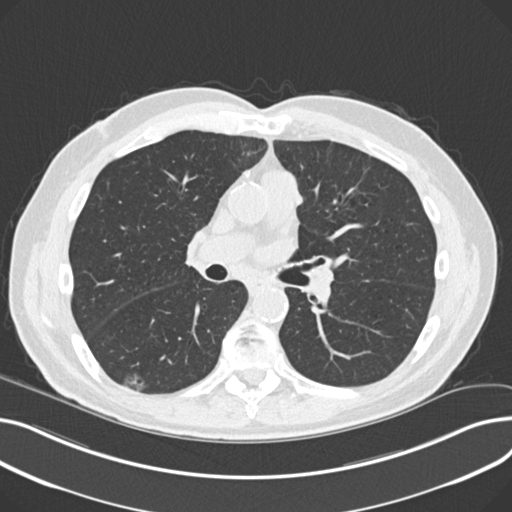
Low-dose screening chest CT, one axial slice; position 122 of 230 along the scan axis; reconstruction kernel B30f; lung window (W 1500 / L -600 HU); 2 mm slice thickness; 512 × 512 image matrix.
Structures marked on this image (outlined manually by an expert reader):
- lesion 1 (nodule, lower lobe of right lung): bounding box (x1, y1, x2, y2) in pixels: (124, 373, 146, 392)